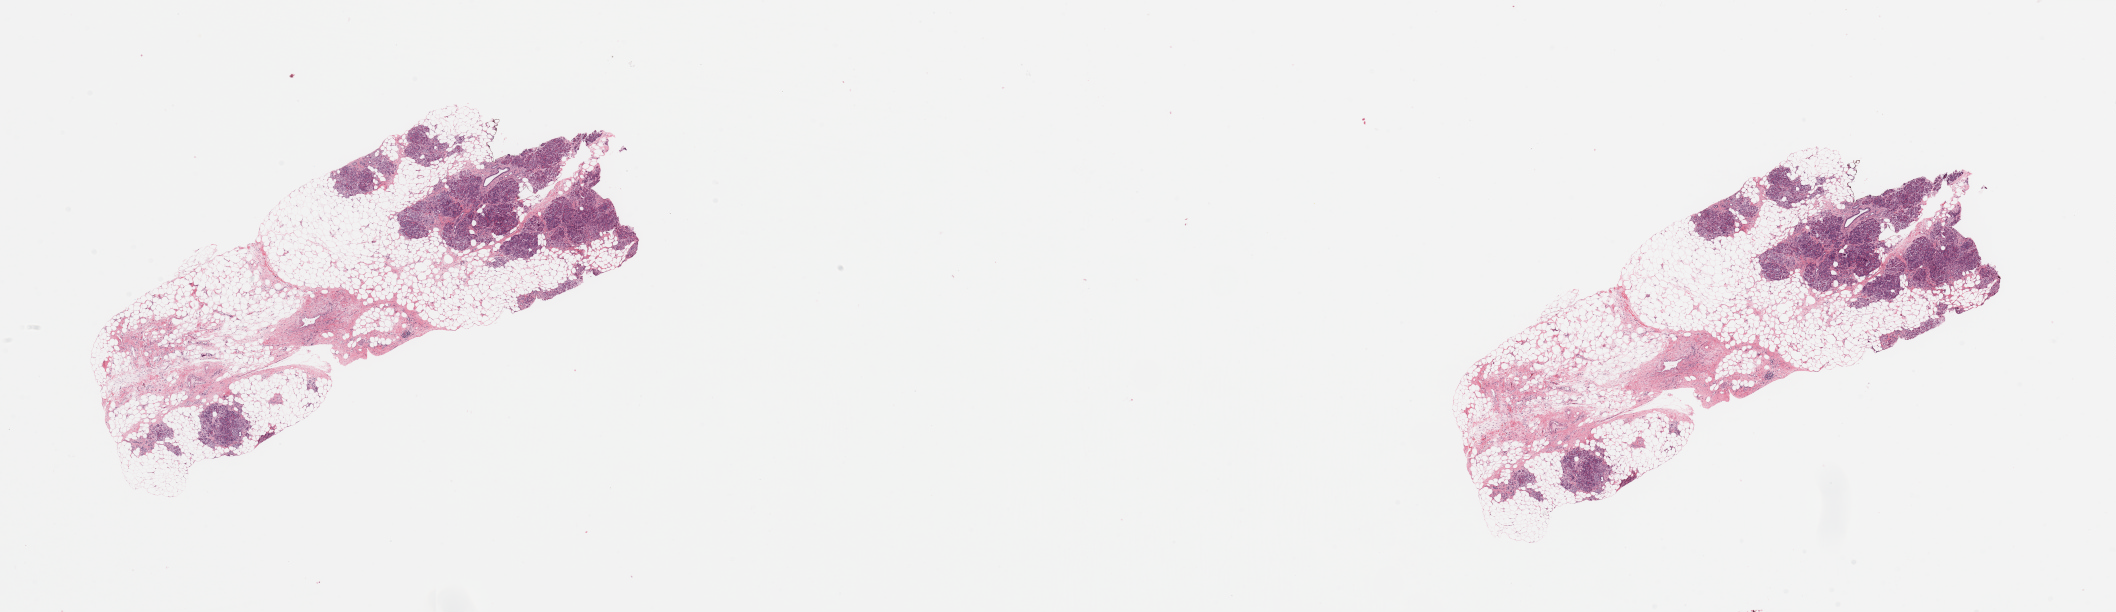
H&E whole-slide image — shown as a low-resolution overview of the whole scanned area (about 33.5 x 9.7 mm, from a 20x scan). Normal (non-tumour) tissue sample, sampled site: pancreas. 80-year-old male patient.
This section: normal (non-tumour) tissue from the same patient. Patient diagnosis: Infiltrating duct carcinoma, NOS.